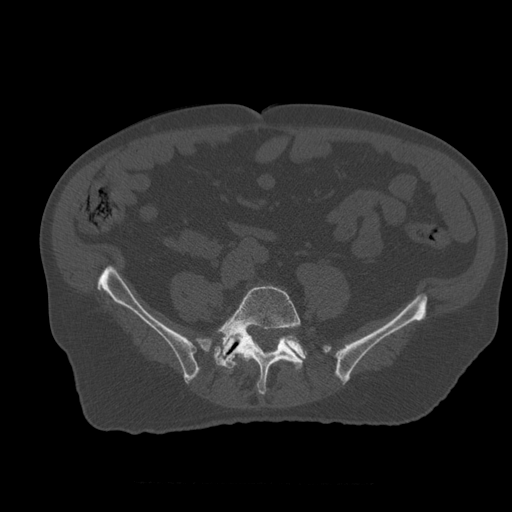
CT including the spine, one axial slice; slice 141 of 399 in the series (ordered by position); reconstruction kernel STANDARD; 120 kVp; bone window (W 1800 / L 400 HU); 1.25 mm slice thickness; 512 × 512 image matrix. Patient age 73 years. From the clinical record (not read from this slice): primary cancer: prostate; vertebrae with lytic lesions (as recorded): L2.
Structures marked on this image (semi-automatic segmentation, software-assisted and operator-edited):
- L4 vertebra: bounding box [x1, y1, x2, y2] px = [241, 353, 254, 361]
- L5 vertebra: [215, 286, 303, 395]